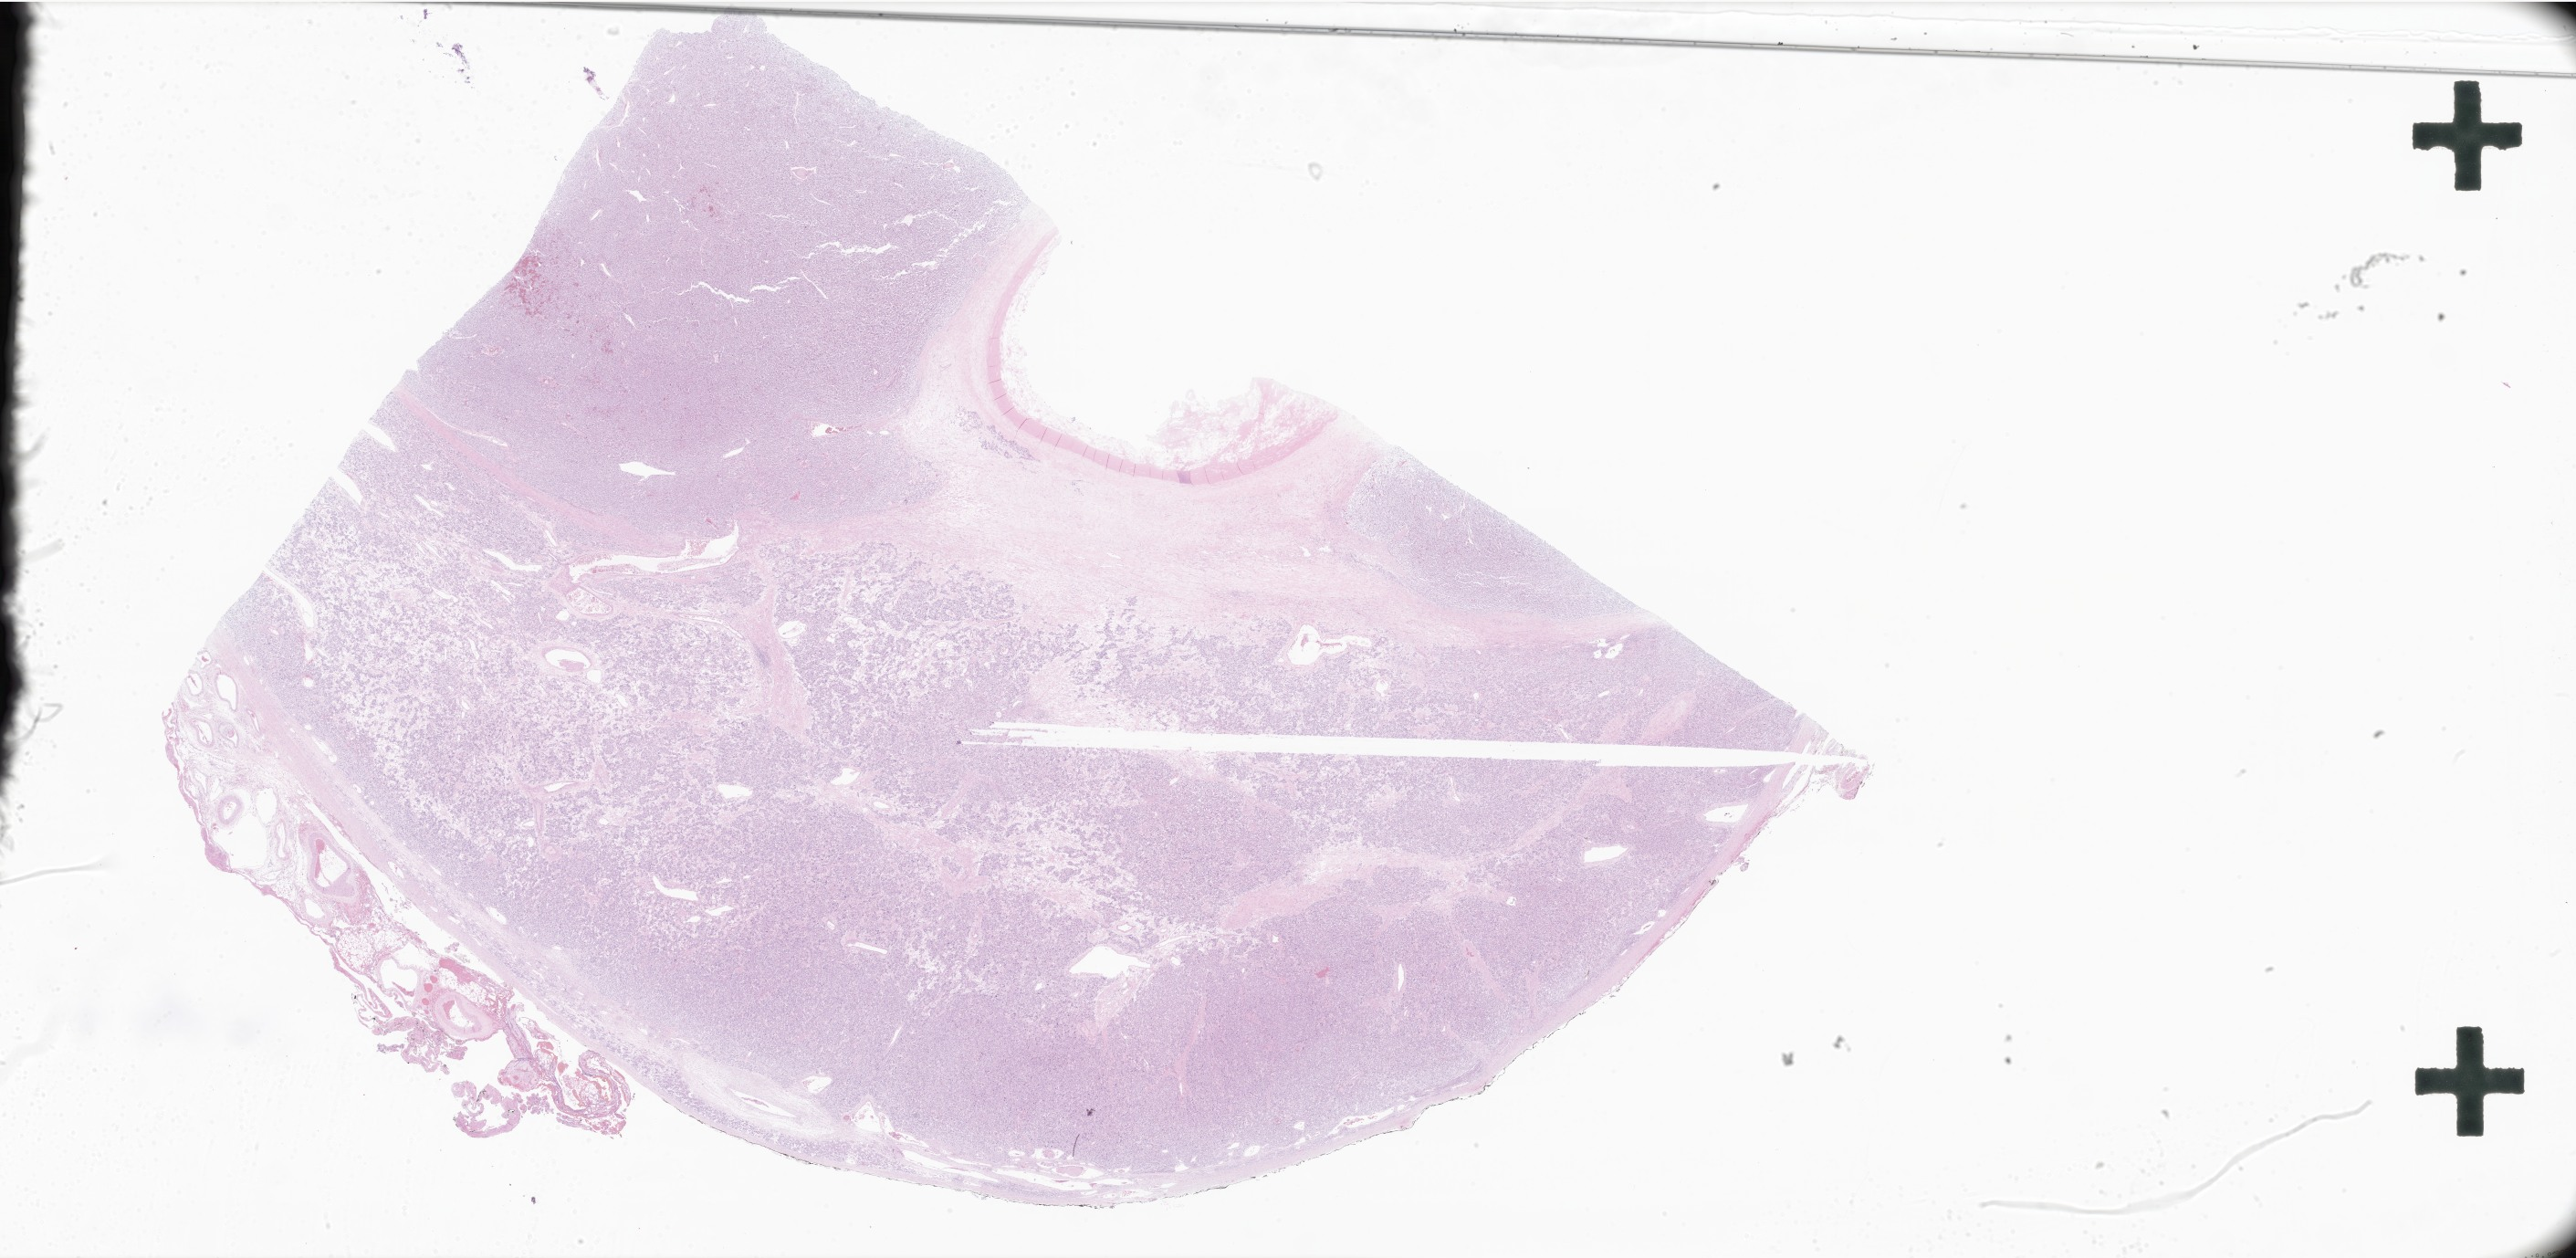
Whole-slide image, haematoxylin and eosin stain of tumor tissue from the adrenal gland — shown as a low-resolution overview of the whole scanned area (about 47.6 x 23.2 mm). Formalin-fixed, paraffin-embedded (FFPE) tissue. Patient: male, age 153 months (12 years 9 months).
Recorded diagnosis: Pheochromocytoma, NOS.